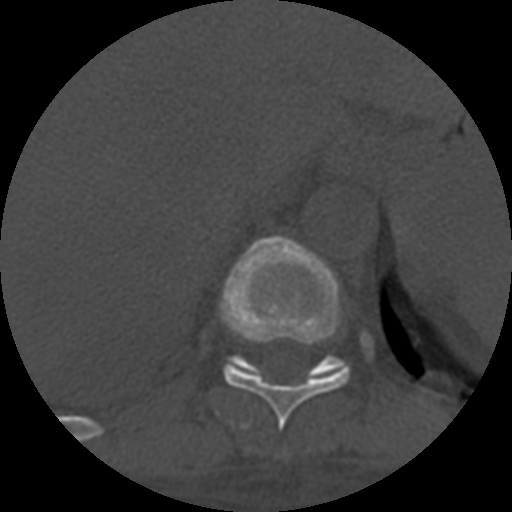
CT including the spine, one axial slice. Position 351 of 708 along the scan axis. Reconstruction kernel STANDARD. One of 3 acquisitions stored at this slice position. Bone window (W 1800 / L 400 HU). 1.25 mm slice thickness. 512 × 512 image matrix, field of view 160 × 160 mm. Patient age 55 years. Case-level facts recorded for this patient, not image findings: primary cancer: colon; vertebrae with lytic lesions (as recorded): T12, L1, L5.
Outlined on this slice (semi-automatically segmented with operator editing):
- T10 vertebra: bounding box <220,237,350,430> (left, top, right, bottom; pixels)
- T11 vertebra: <225,356,349,380>